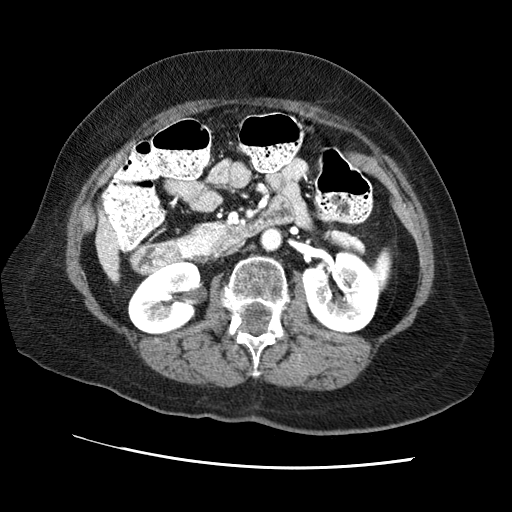
Contrast-enhanced abdominal CT (liver protocol), one axial slice. 120 kVp. Soft-tissue window (W 400 / L 40 HU). 512 × 512 image matrix, field of view 340 × 340 mm. Case-level facts recorded for this patient, not image findings: diagnosis: hepatocellular carcinoma (patient treated with transarterial chemoembolisation; whether this scan precedes or follows treatment is not stated here); TNM stage (as recorded): Stage-II; Child-Pugh class: A; tumour differentiation: no biopsy; tumour nodularity: multinodular.
Annotated regions visible in this slice (semi-automatically segmented with operator editing):
- liver parenchyma outside the tumour (the mass and vessels are separate outlines, so this box may not span the whole liver): box from (x=96, y=216) to (x=118, y=280) px
- liver vessels: (x=105, y=234)–(x=114, y=267)